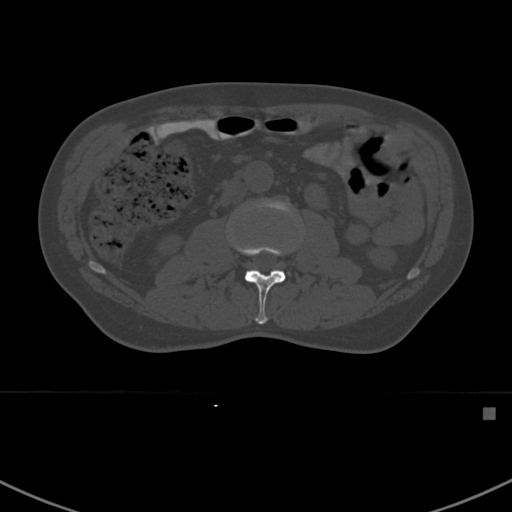
CT including the spine, one axial slice. Slice 279 of 412 in the series (ordered by position). Reconstruction kernel Br40s. 120 kVp. Bone window (W 1800 / L 400 HU). 1.5 mm slice thickness. 512 × 512 image matrix, field of view 358 × 358 mm. Male patient, age 59 years. Case-level facts recorded for this patient, not image findings: primary cancer: prostate.
Outlined on this slice (semi-automatic segmentation, software-assisted and operator-edited):
- L2 vertebra: bounding box <230,238,292,324> (left, top, right, bottom; pixels)
- L3 vertebra: <252,199,293,214>